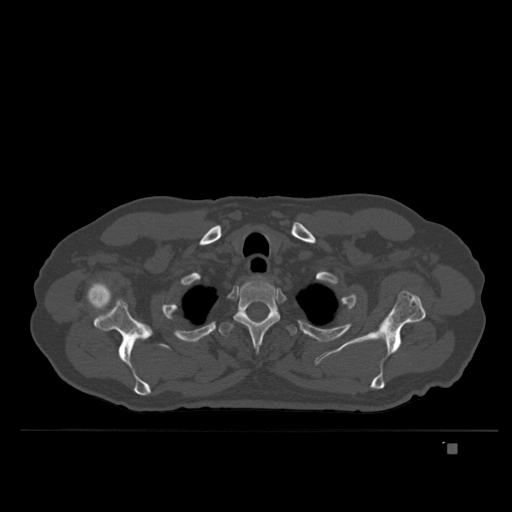
CT including the spine, one axial slice. Slice 311 of 435 in the series (ordered by position). Bone window (W 1800 / L 400 HU). 1.5 mm slice thickness. 512 × 512 image matrix, field of view 434 × 434 mm. Male patient, age 73 years. From the clinical record (not read from this slice): primary cancer: skin.
Outlined on this slice (semi-automatically segmented with operator editing):
- T2 vertebra: bounding box <233,281,280,350> (left, top, right, bottom; pixels)
- T3 vertebra: <219,310,297,338>